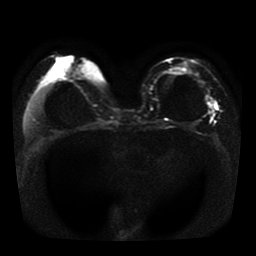
Breast MRI, one axial slice. Slice 15 of 41 in the series (ordered by position). Diffusion-weighted series; image 2 of 4 stored at this slice position (different b-values; order by instance number). 1.5 T. 5 mm slice thickness. 256 × 256 image matrix, field of view 330 × 330 mm. Female patient.
Outlined on this slice (outlined manually by an expert reader):
- tumour on diffusion-weighted imaging: bounding box <209,103,217,110> (left, top, right, bottom; pixels)